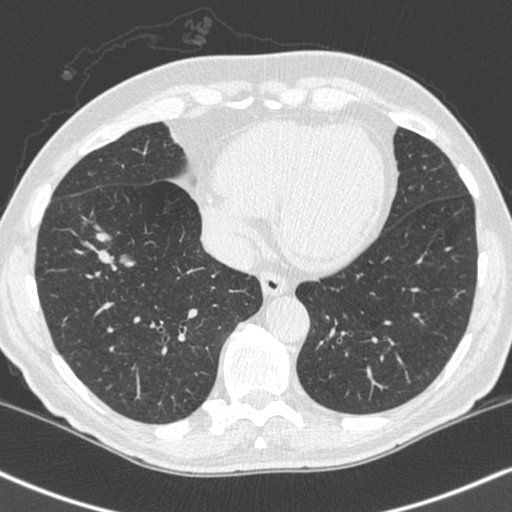
Low-dose screening chest CT, axial slice, first (baseline) screen, lung window (W 1500 / L -600 HU), 1.3 mm slice thickness, standard (soft-tissue) reconstruction kernel (C), 512 × 512 image matrix. Male participant, aged 68 years at enrolment. Current smoker at enrolment.
Lesion marked by an expert reader, bounding box (x1, y1, x2, y2) in pixels: (76, 200, 152, 270). The exam's reader record, not a measurement of the box and not confirmed to be the same lesion: non-calcified nodule or mass ≥4 mm, right lower lobe, 34 × 17 mm, smooth margins, soft tissue attenuation.